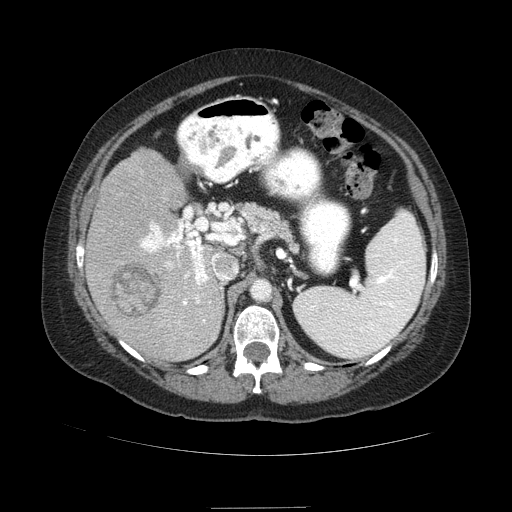
Contrast-enhanced abdominal CT (liver protocol), one axial slice; slice 50 of 89 in the series (ordered by position); reconstruction kernel STANDARD; 120 kVp; soft-tissue window (W 400 / L 40 HU); 512 × 512 image matrix, field of view 400 × 400 mm. Case-level facts recorded for this patient, not image findings: diagnosis: hepatocellular carcinoma (patient treated with transarterial chemoembolisation; whether this scan precedes or follows treatment is not stated here); TNM stage (as recorded): Stage-IIIB; Child-Pugh class: A.
Structures marked on this image (semi-automatically segmented with operator editing):
- liver parenchyma outside the tumour (the mass and vessels are separate outlines, so this box may not span the whole liver): bounding box [x1, y1, x2, y2] px = [86, 148, 236, 360]
- mass: [109, 261, 161, 316]
- liver vessels: [140, 222, 220, 323]